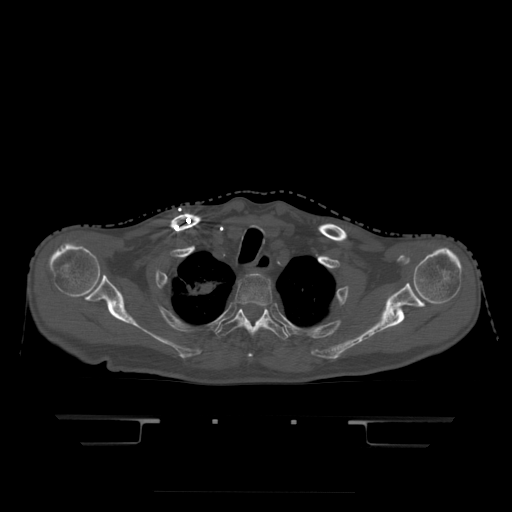
CT including the spine, one axial slice. Slice 378 of 522 in the series (ordered by position). Bone window (W 1800 / L 400 HU). 1.25 mm slice thickness. 512 × 512 image matrix, field of view 436 × 436 mm. Patient age 68 years. From the clinical record (not read from this slice): primary cancer: urothelial.
Structures marked on this image (semi-automatic segmentation, software-assisted and operator-edited):
- T2 vertebra: bounding box <235,274,273,357> (left, top, right, bottom; pixels)
- T3 vertebra: <216,306,288,340>